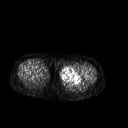
FDG PET of an extremity soft-tissue mass (from a PET/CT study), one axial slice. Position 231 of 267 along the scan axis. 3.27 mm slice thickness. 128 × 128 image matrix, field of view 500 × 500 mm. Female patient, age 42 years. Case-level facts recorded for this patient, not image findings: histological type: pleiomorphic leiomyosarcoma; grade: intermediate; site of the primary tumour: left thigh.
Annotated regions visible in this slice (expert contour drawn on MRI and transferred to this co-registered scan by the dataset authors):
- gross tumour volume including surrounding oedema: bounding box <60,66,83,84> (left, top, right, bottom; pixels)
- gross tumour volume (mass): <60,67,81,84>